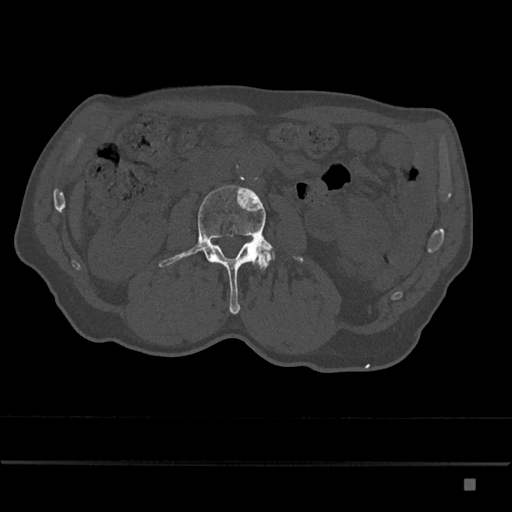
CT including the spine, one axial slice; position 406 of 797 along the scan axis; bone window (W 1800 / L 400 HU); 0.5 mm slice thickness; 512 × 512 image matrix. Patient: male, 72 years. Case-level facts recorded for this patient, not image findings: primary cancer: prostate.
Structures marked on this image (semi-automatically segmented with operator editing):
- L3 vertebra: bounding box (x1, y1, x2, y2) in pixels: (158, 185, 304, 314)
- L4 vertebra: (257, 250, 273, 270)